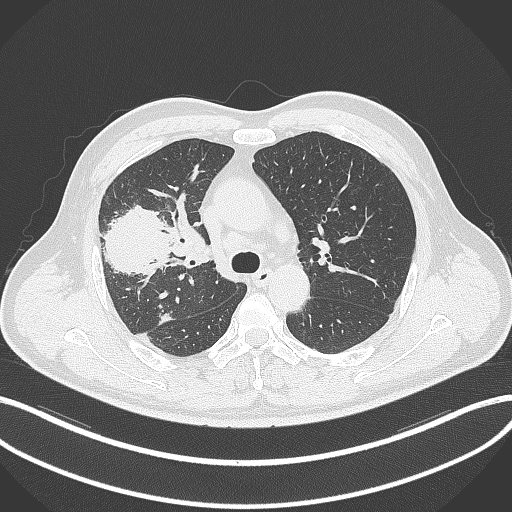
Chest CT, one axial slice. Position 224 of 348 along the scan axis. Reconstruction kernel B70f. 120 kVp. Lung window (W 1500 / L -600 HU). 1 mm slice thickness. 512 × 512 image matrix, field of view 400 × 400 mm. Male patient, age 55 years. From the clinical record (not read from this slice): clinical TNM (as recorded): T3 N2 M1.
Annotated regions visible in this slice (bounding box drawn by a radiologist):
- lung tumour (recorded histology: adenocarcinoma): bounding box [x1, y1, x2, y2] px = [96, 205, 171, 280]